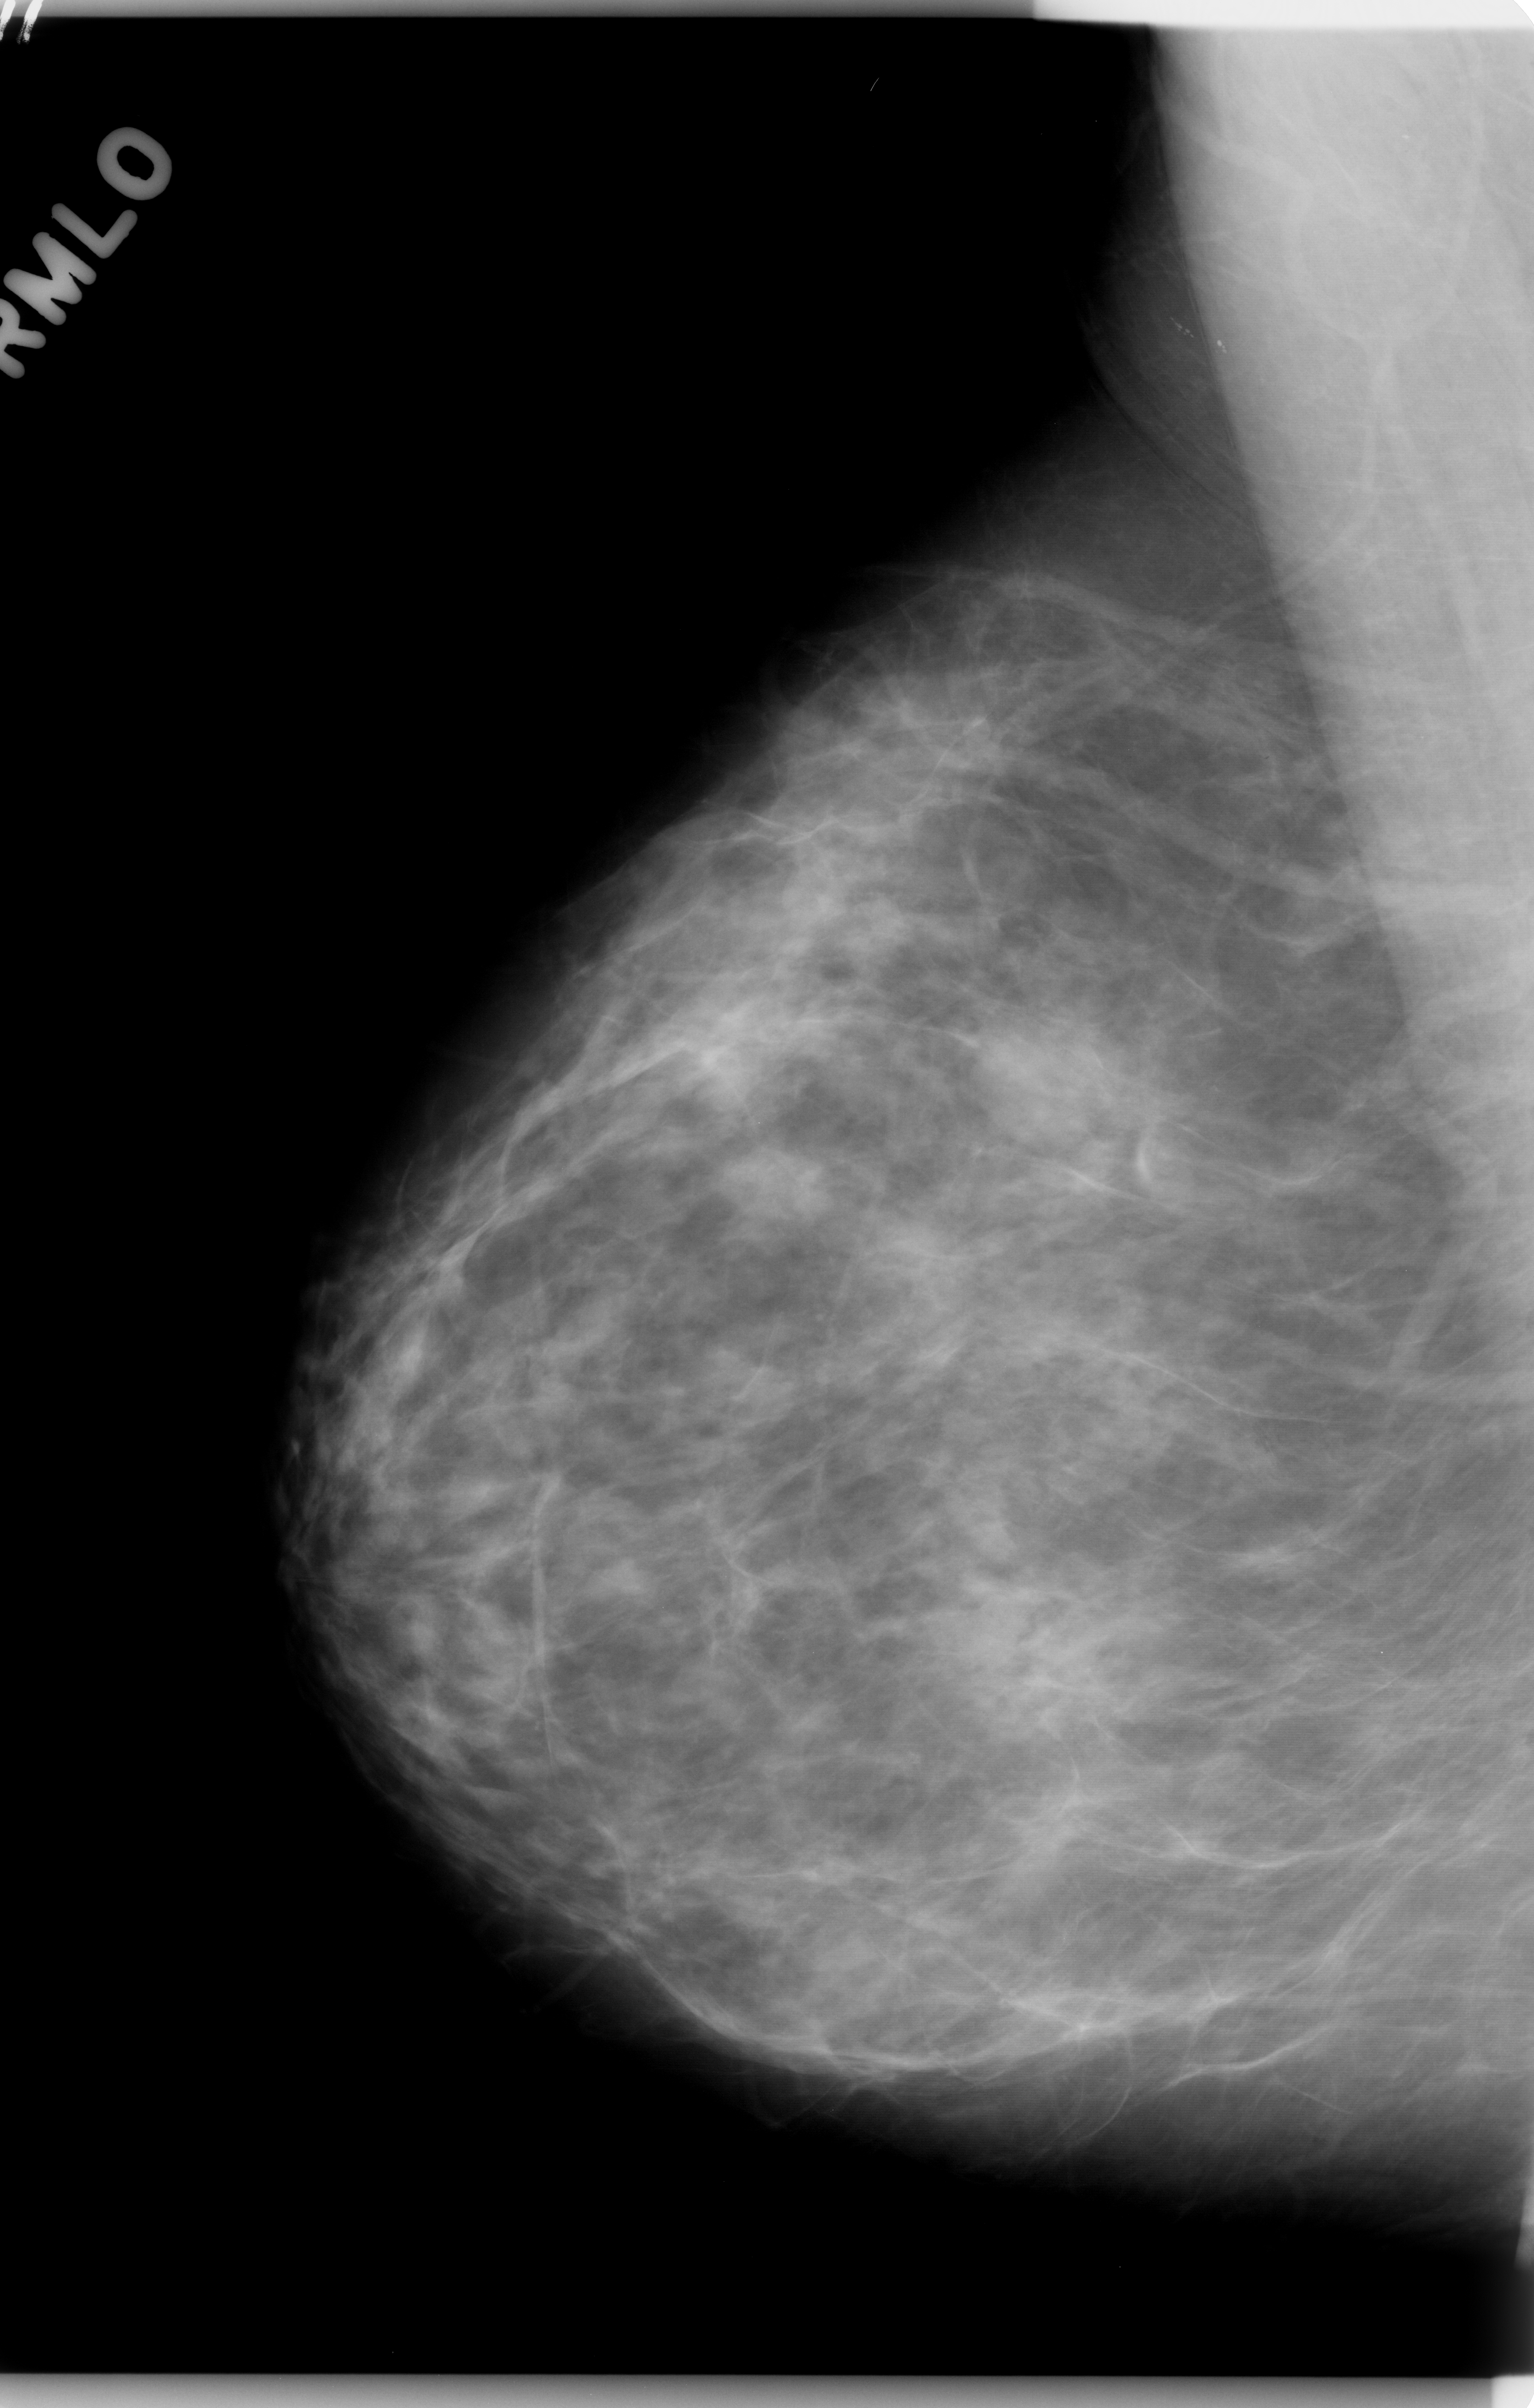
Scanned film-screen mammogram, right breast, mediolateral oblique (MLO) view, BI-RADS breast density category 2 (scale 1–4).
Abnormality record for this image: mass, shape oval, margins circumscribed; BI-RADS assessment category 4; pathology result (as recorded, not read from the image): benign.